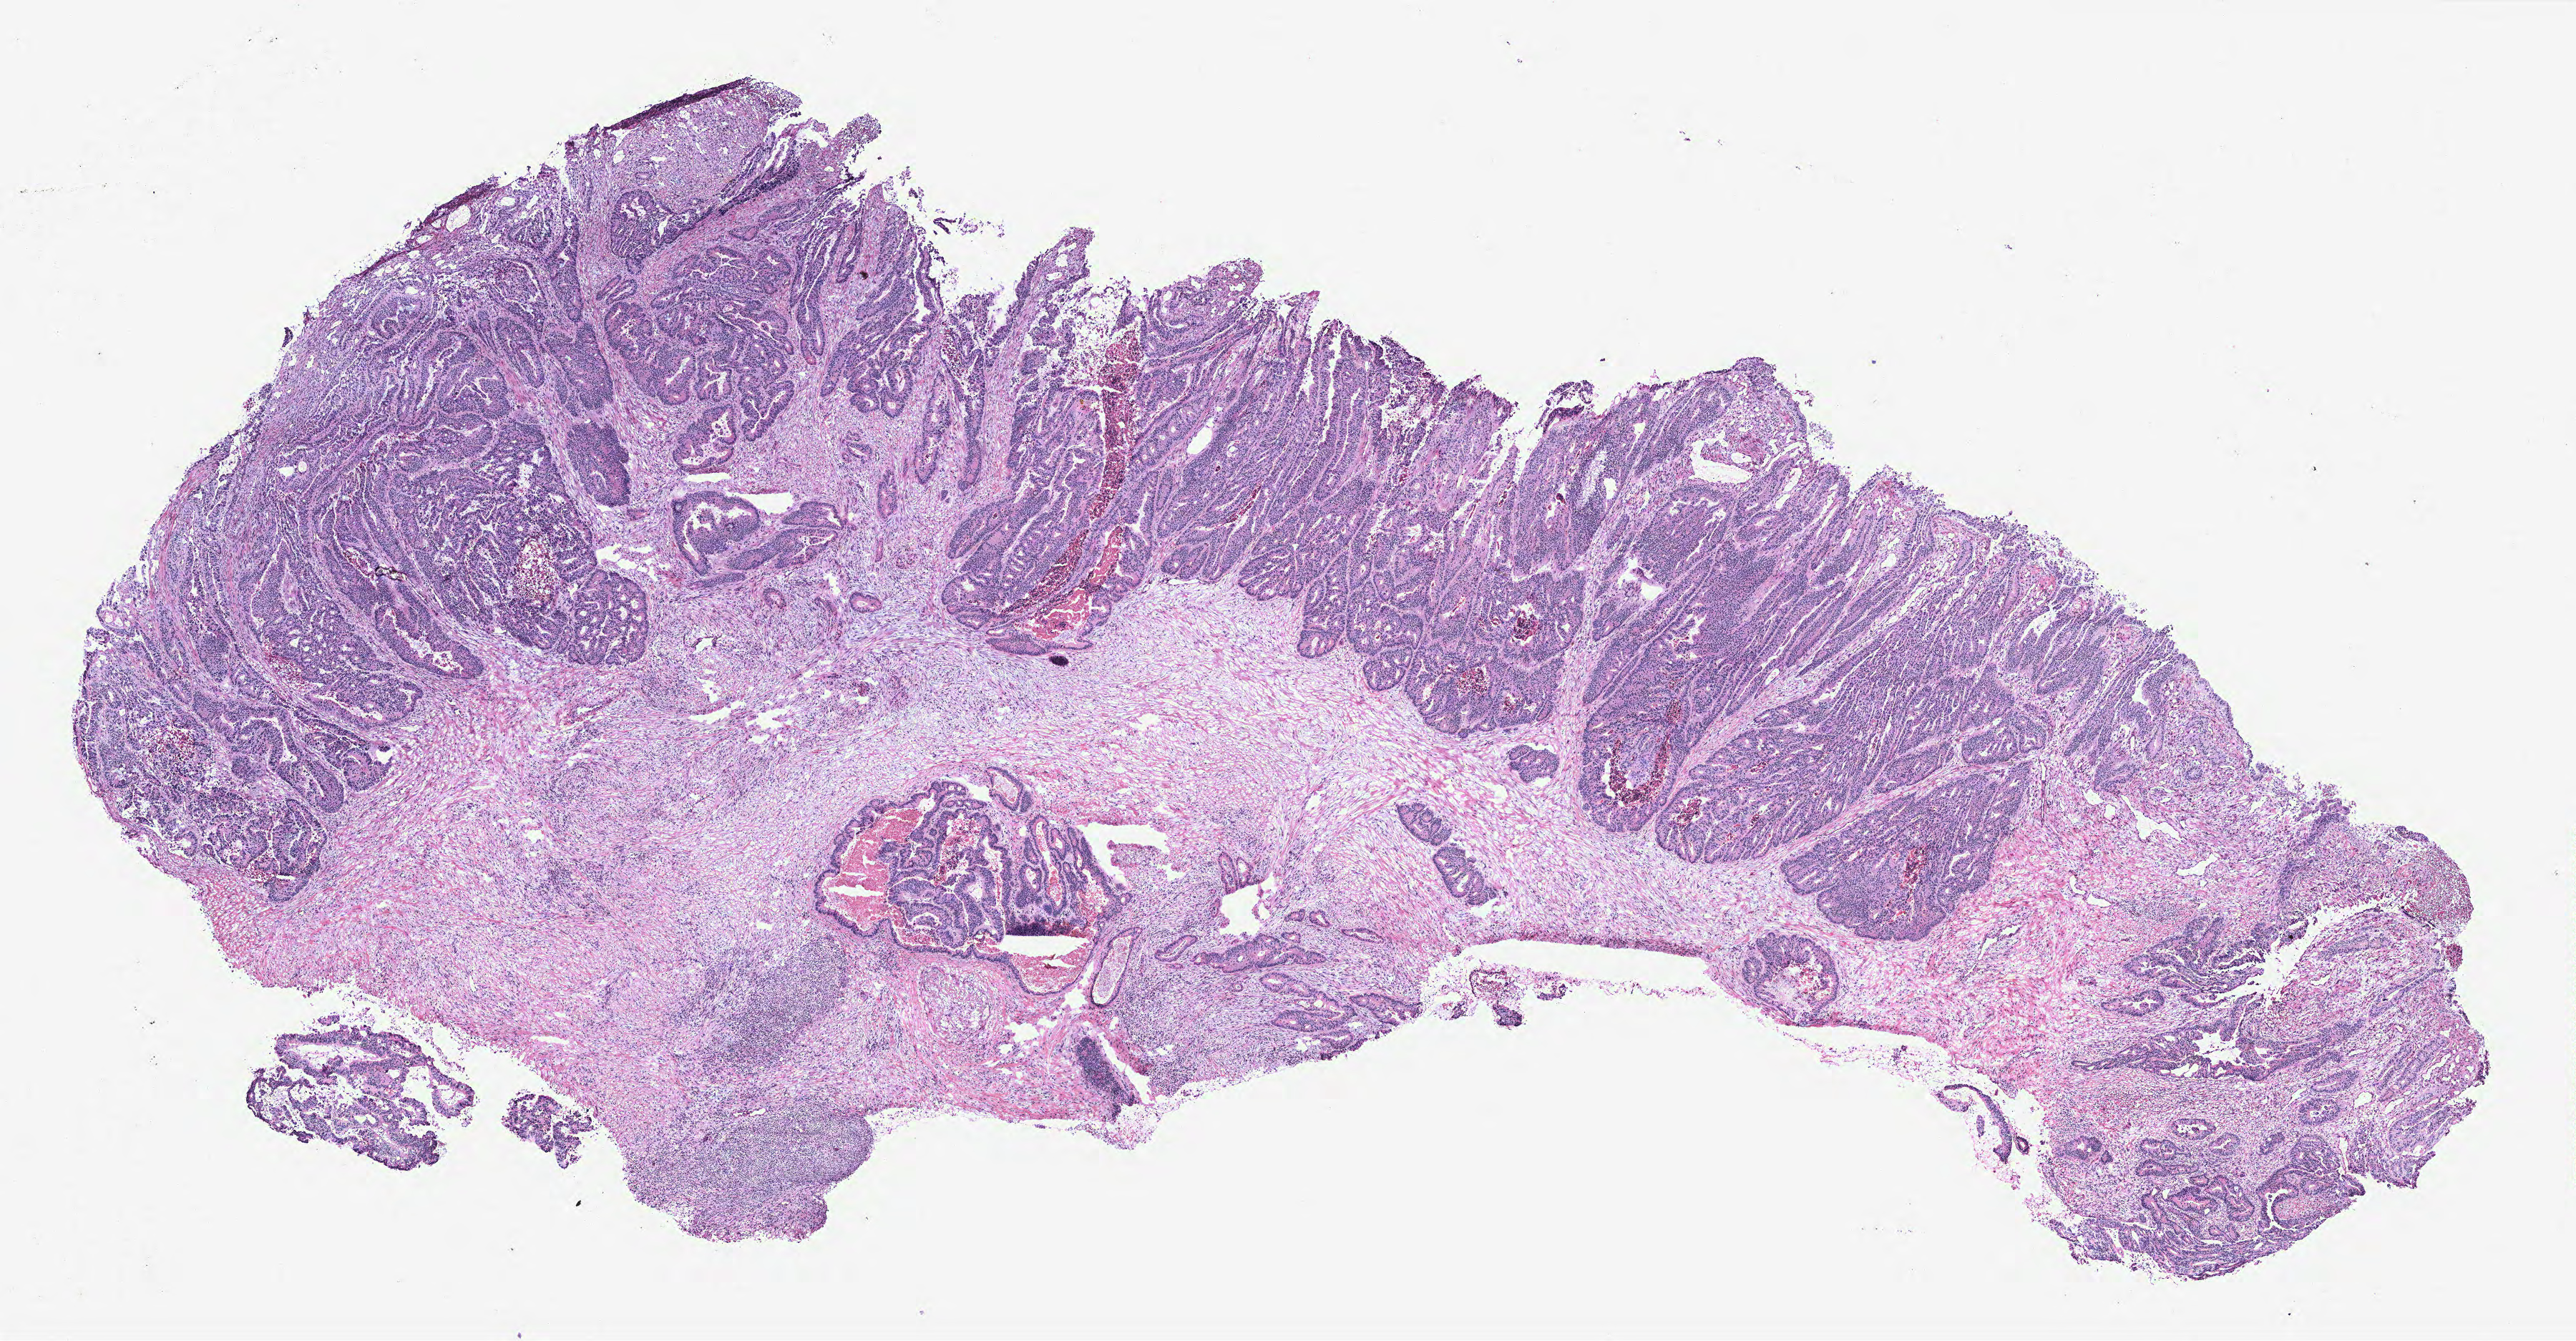
Whole-slide histology image, Hematoxylin and eosin (H&E) stained, low-resolution overview of the scanned area, about 14.4 x 7.5 mm; normal (non-tumour) tissue sample, colon. Patient: male, age 87 years.
This section: normal (non-tumour) tissue from the same patient. Patient diagnosis: Adenocarcinoma, NOS.